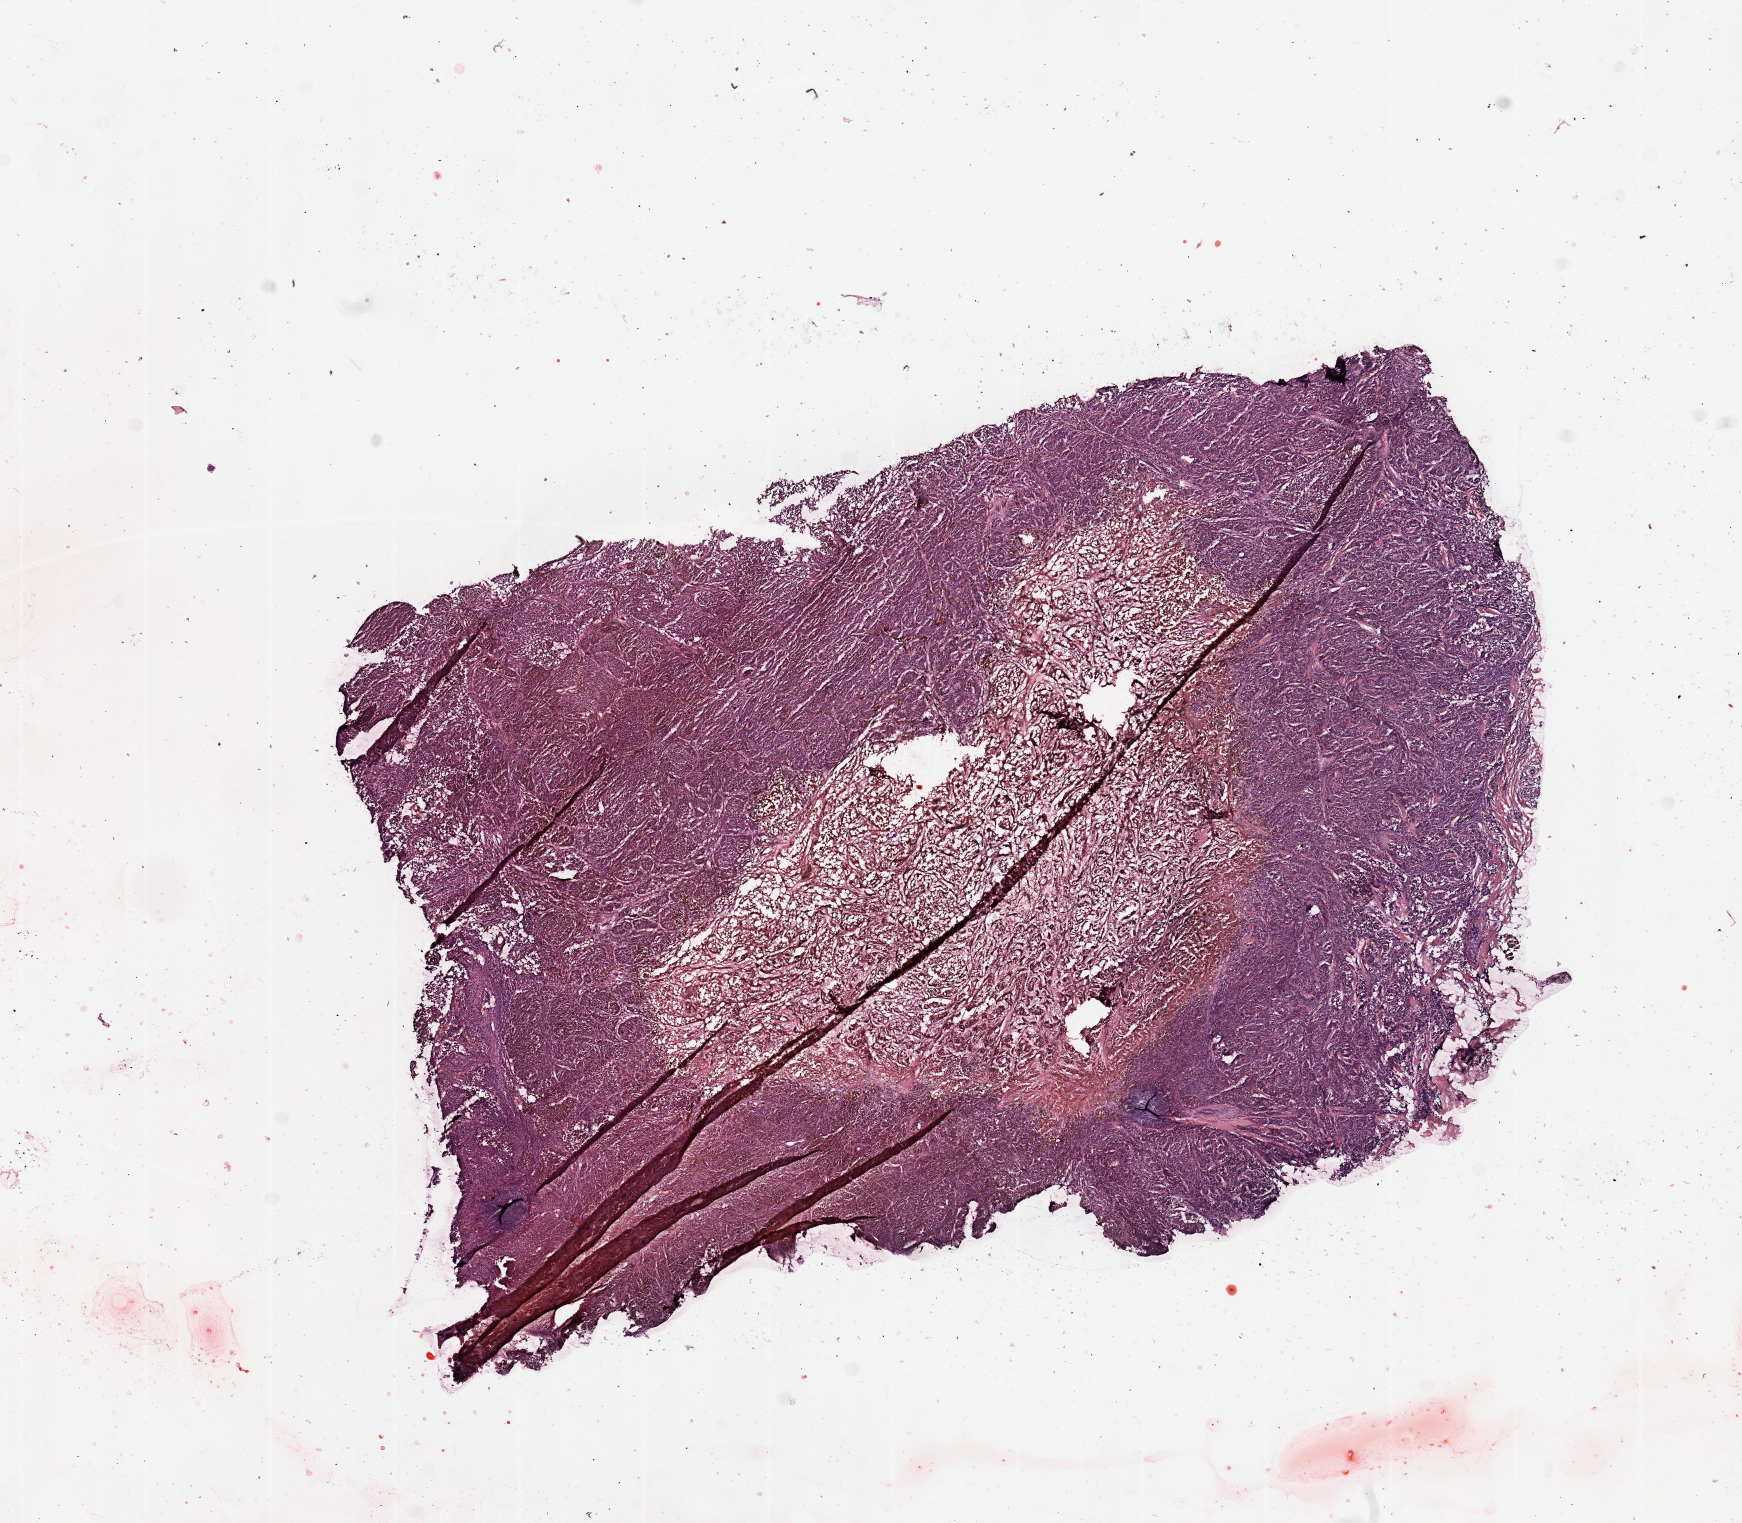
Whole-slide histology image, H&E — whole scanned area (about 13.8 x 12.0 mm) shown as a low-resolution overview; melanoma tumour tissue; sampled site not recorded. Male, 54 y/o.
Patient diagnosis (cohort enrolment): cutaneous melanoma (skin). Primary tumour site (as recorded): trunk.